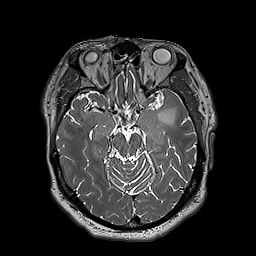
Brain MRI from a brain-tumour surgery series, one axial slice. Slice 122 of 192 in the series (ordered by position). 1 mm slice thickness. 256 × 256 image matrix. From the clinical record (not read from this slice): histopathology: Astrocytoma; WHO grade: 3; IDH mutation: yes; tumour location: Left Insular.
Annotated regions visible in this slice (outlined manually by an expert reader):
- tumour: box from (x=154, y=107) to (x=175, y=124) px